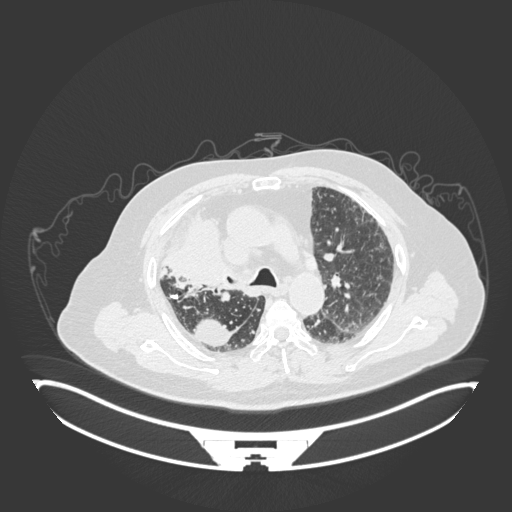
Chest CT, one axial slice; position 123 of 201 along the scan axis; reconstruction kernel B30f; lung window (W 1500 / L -600 HU); 1 mm slice thickness; 512 × 512 image matrix, field of view 500 × 500 mm. Patient: male, 69 years. From the clinical record (not read from this slice): clinical TNM (as recorded): T4 N3 M1.
Annotated regions visible in this slice (bounding box drawn by a radiologist):
- lung tumour (recorded histology: adenocarcinoma): box from (x=156, y=211) to (x=238, y=301) px